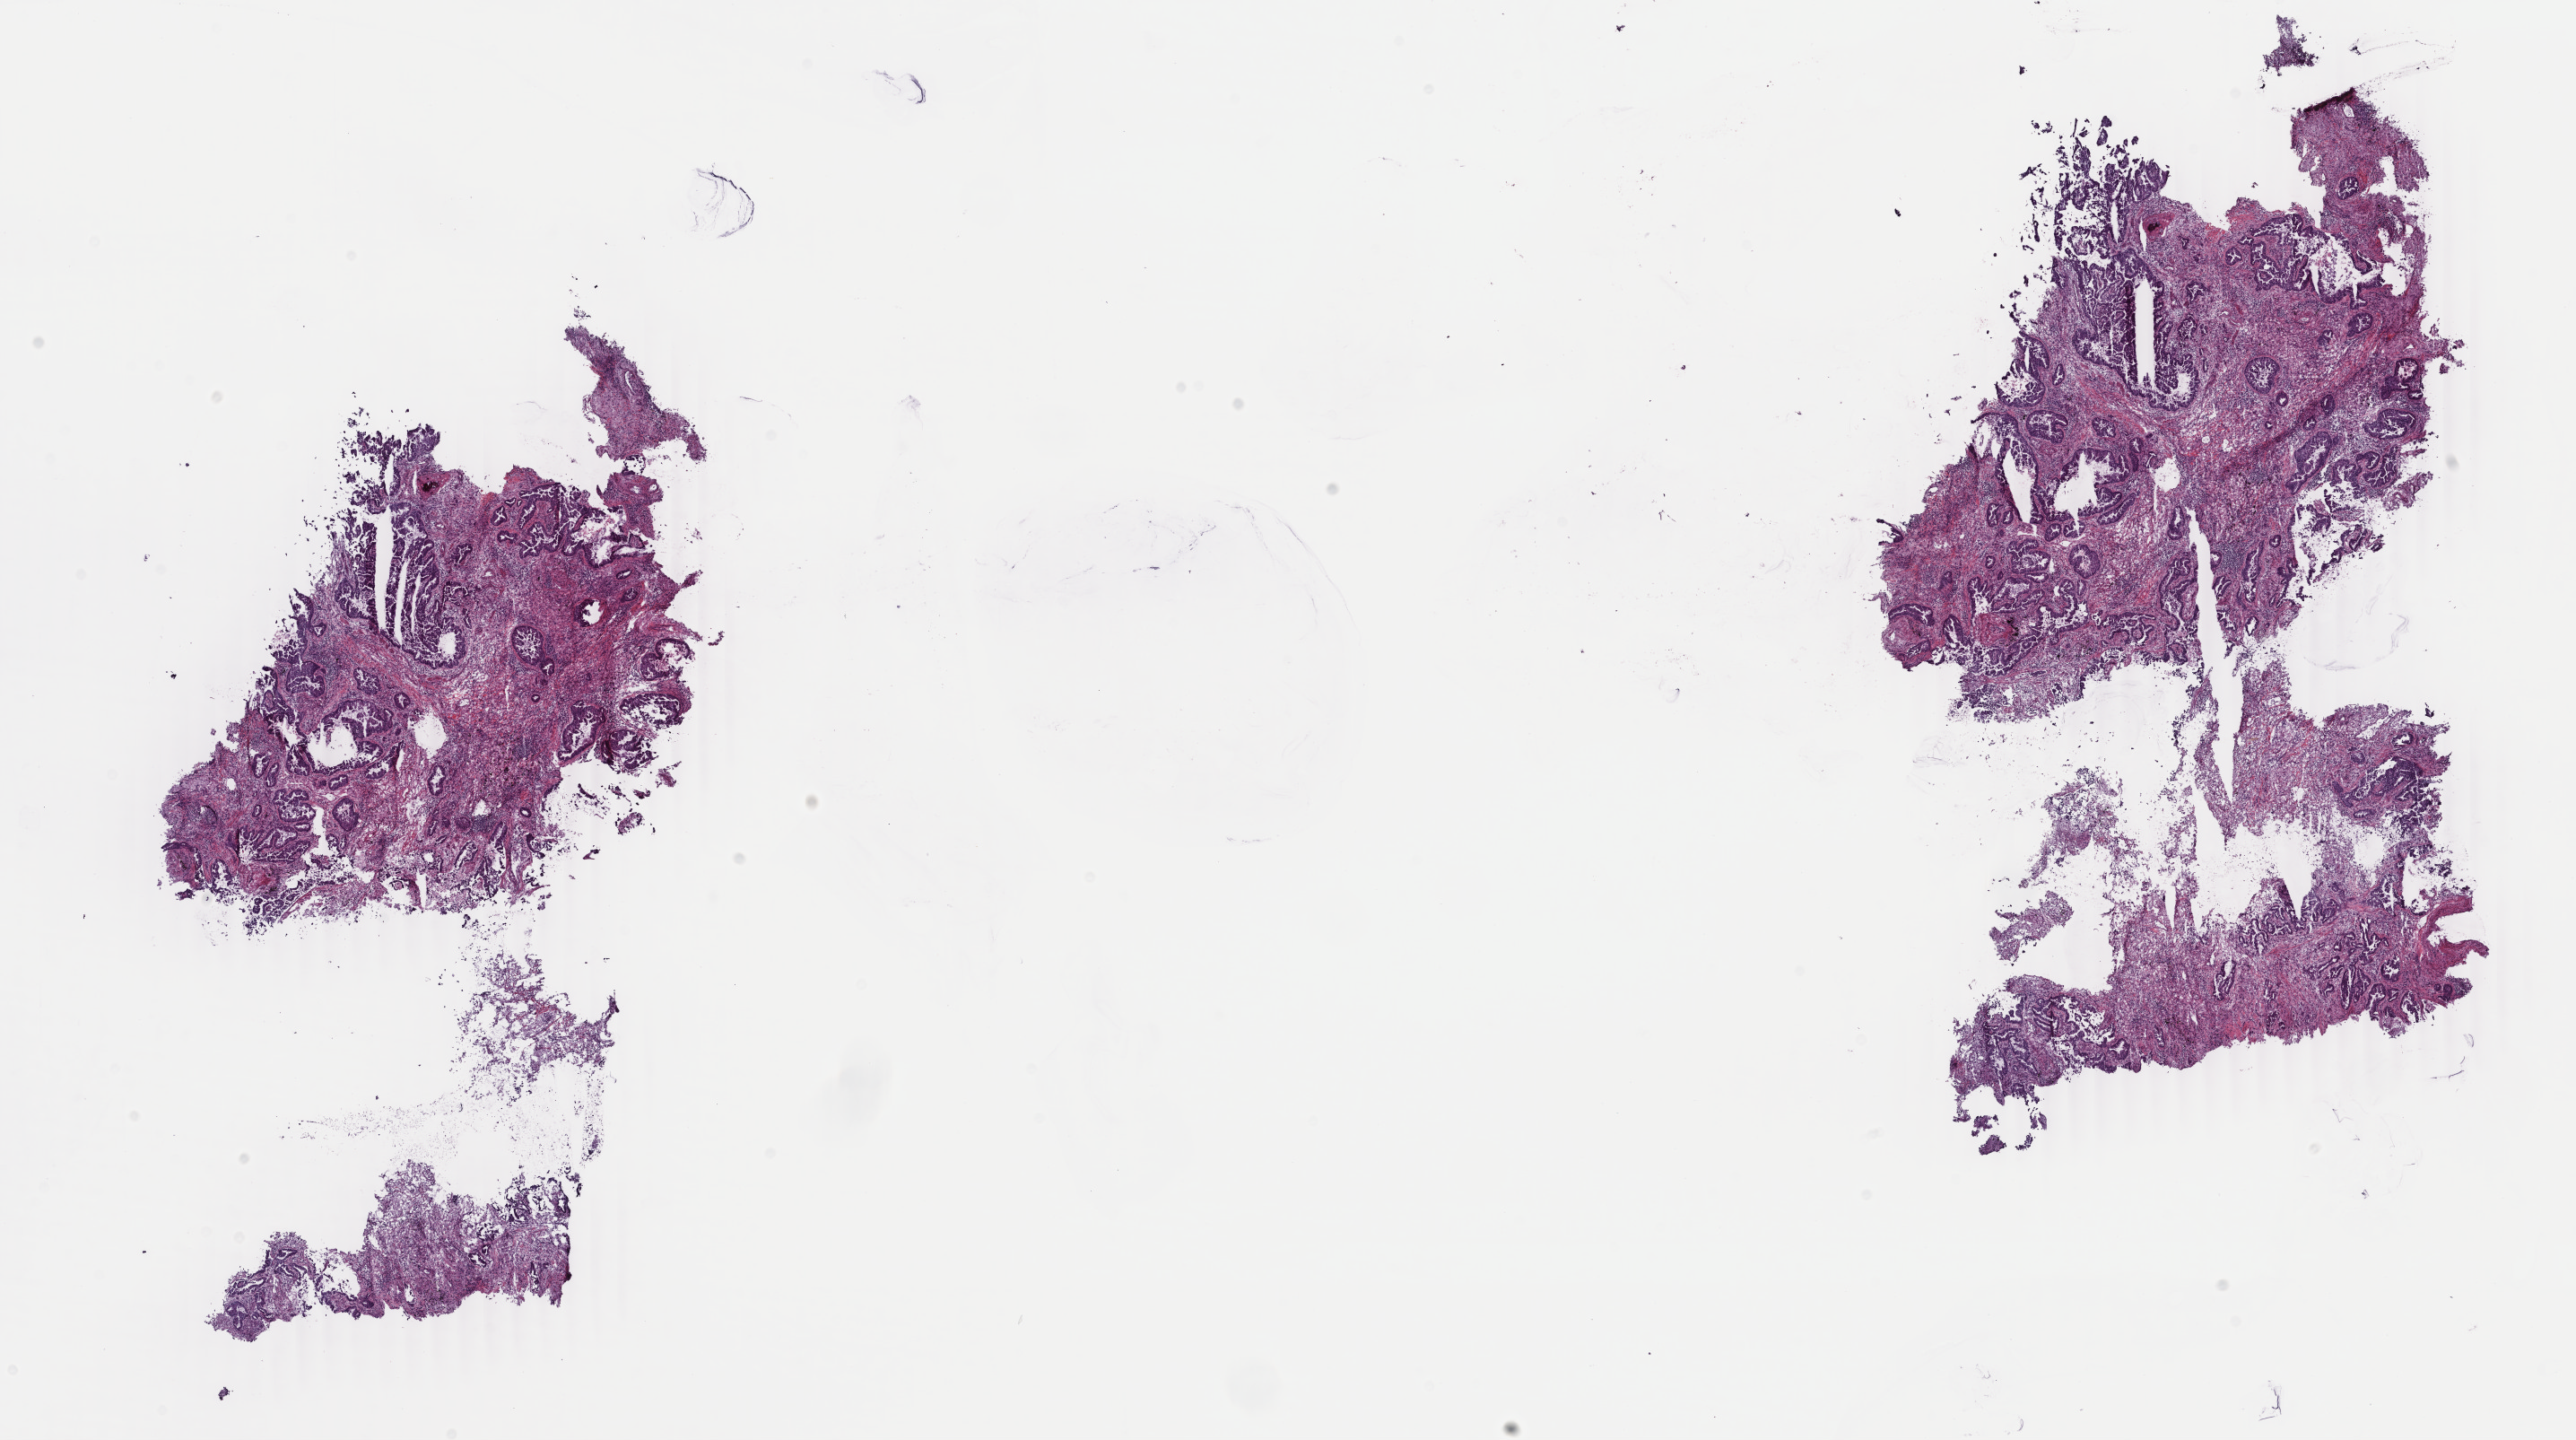
Whole-slide histology image, Hematoxylin and eosin (H&E) stained — a low-resolution overview of the entire scanned area, about 22.8 x 12.8 mm. Frozen section. Lung, primary tumour sample. Patient: male, age at initial diagnosis 71 years. Slide review estimates, as recorded: tumour cells 35%, tumour nuclei 90%, normal cells 0%, stromal cells 65%, necrosis 0%. Inflammatory infiltration, as recorded: lymphocyte infiltration 15%, monocyte infiltration 2%, neutrophil infiltration 0%.
• AJCC pathologic stage: IIIA
• laterality: left
• histologic diagnosis: Adenocarcinoma, NOS (lower lobe, lung)